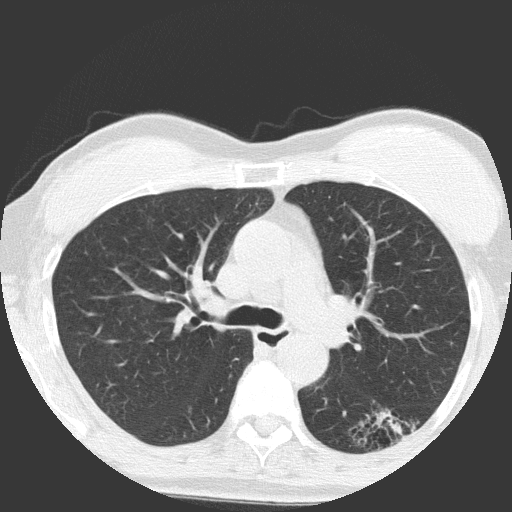
Low-dose screening chest CT, axial slice, baseline screening round, lung window (W 1500 / L -600 HU), 2 mm slice thickness, lung (sharp) reconstruction kernel (FC51), slice 53 of 149 in the series. Female, age 64 years at enrolment. Former smoker at enrolment.
Expert reader's lesion annotation, bounding box (x1, y1, x2, y2) in pixels: (337, 393, 424, 464). Reader record for this screening exam (exam-level; its link to the box is not recorded): non-calcified nodule or mass ≥4 mm, right upper lobe, 4 × 4 mm, poorly defined margins, ground glass attenuation. Note: the box lies in the patient's left hemithorax on this image, whereas the reader's record names the right lung; they may be different findings. Participant outcome: lung cancer diagnosed 932 days after this screen — adenocarcinoma, NOS, left lower lobe, moderately differentiated (G2), stage IA (AJCC 6th edition), 17 mm at pathology.